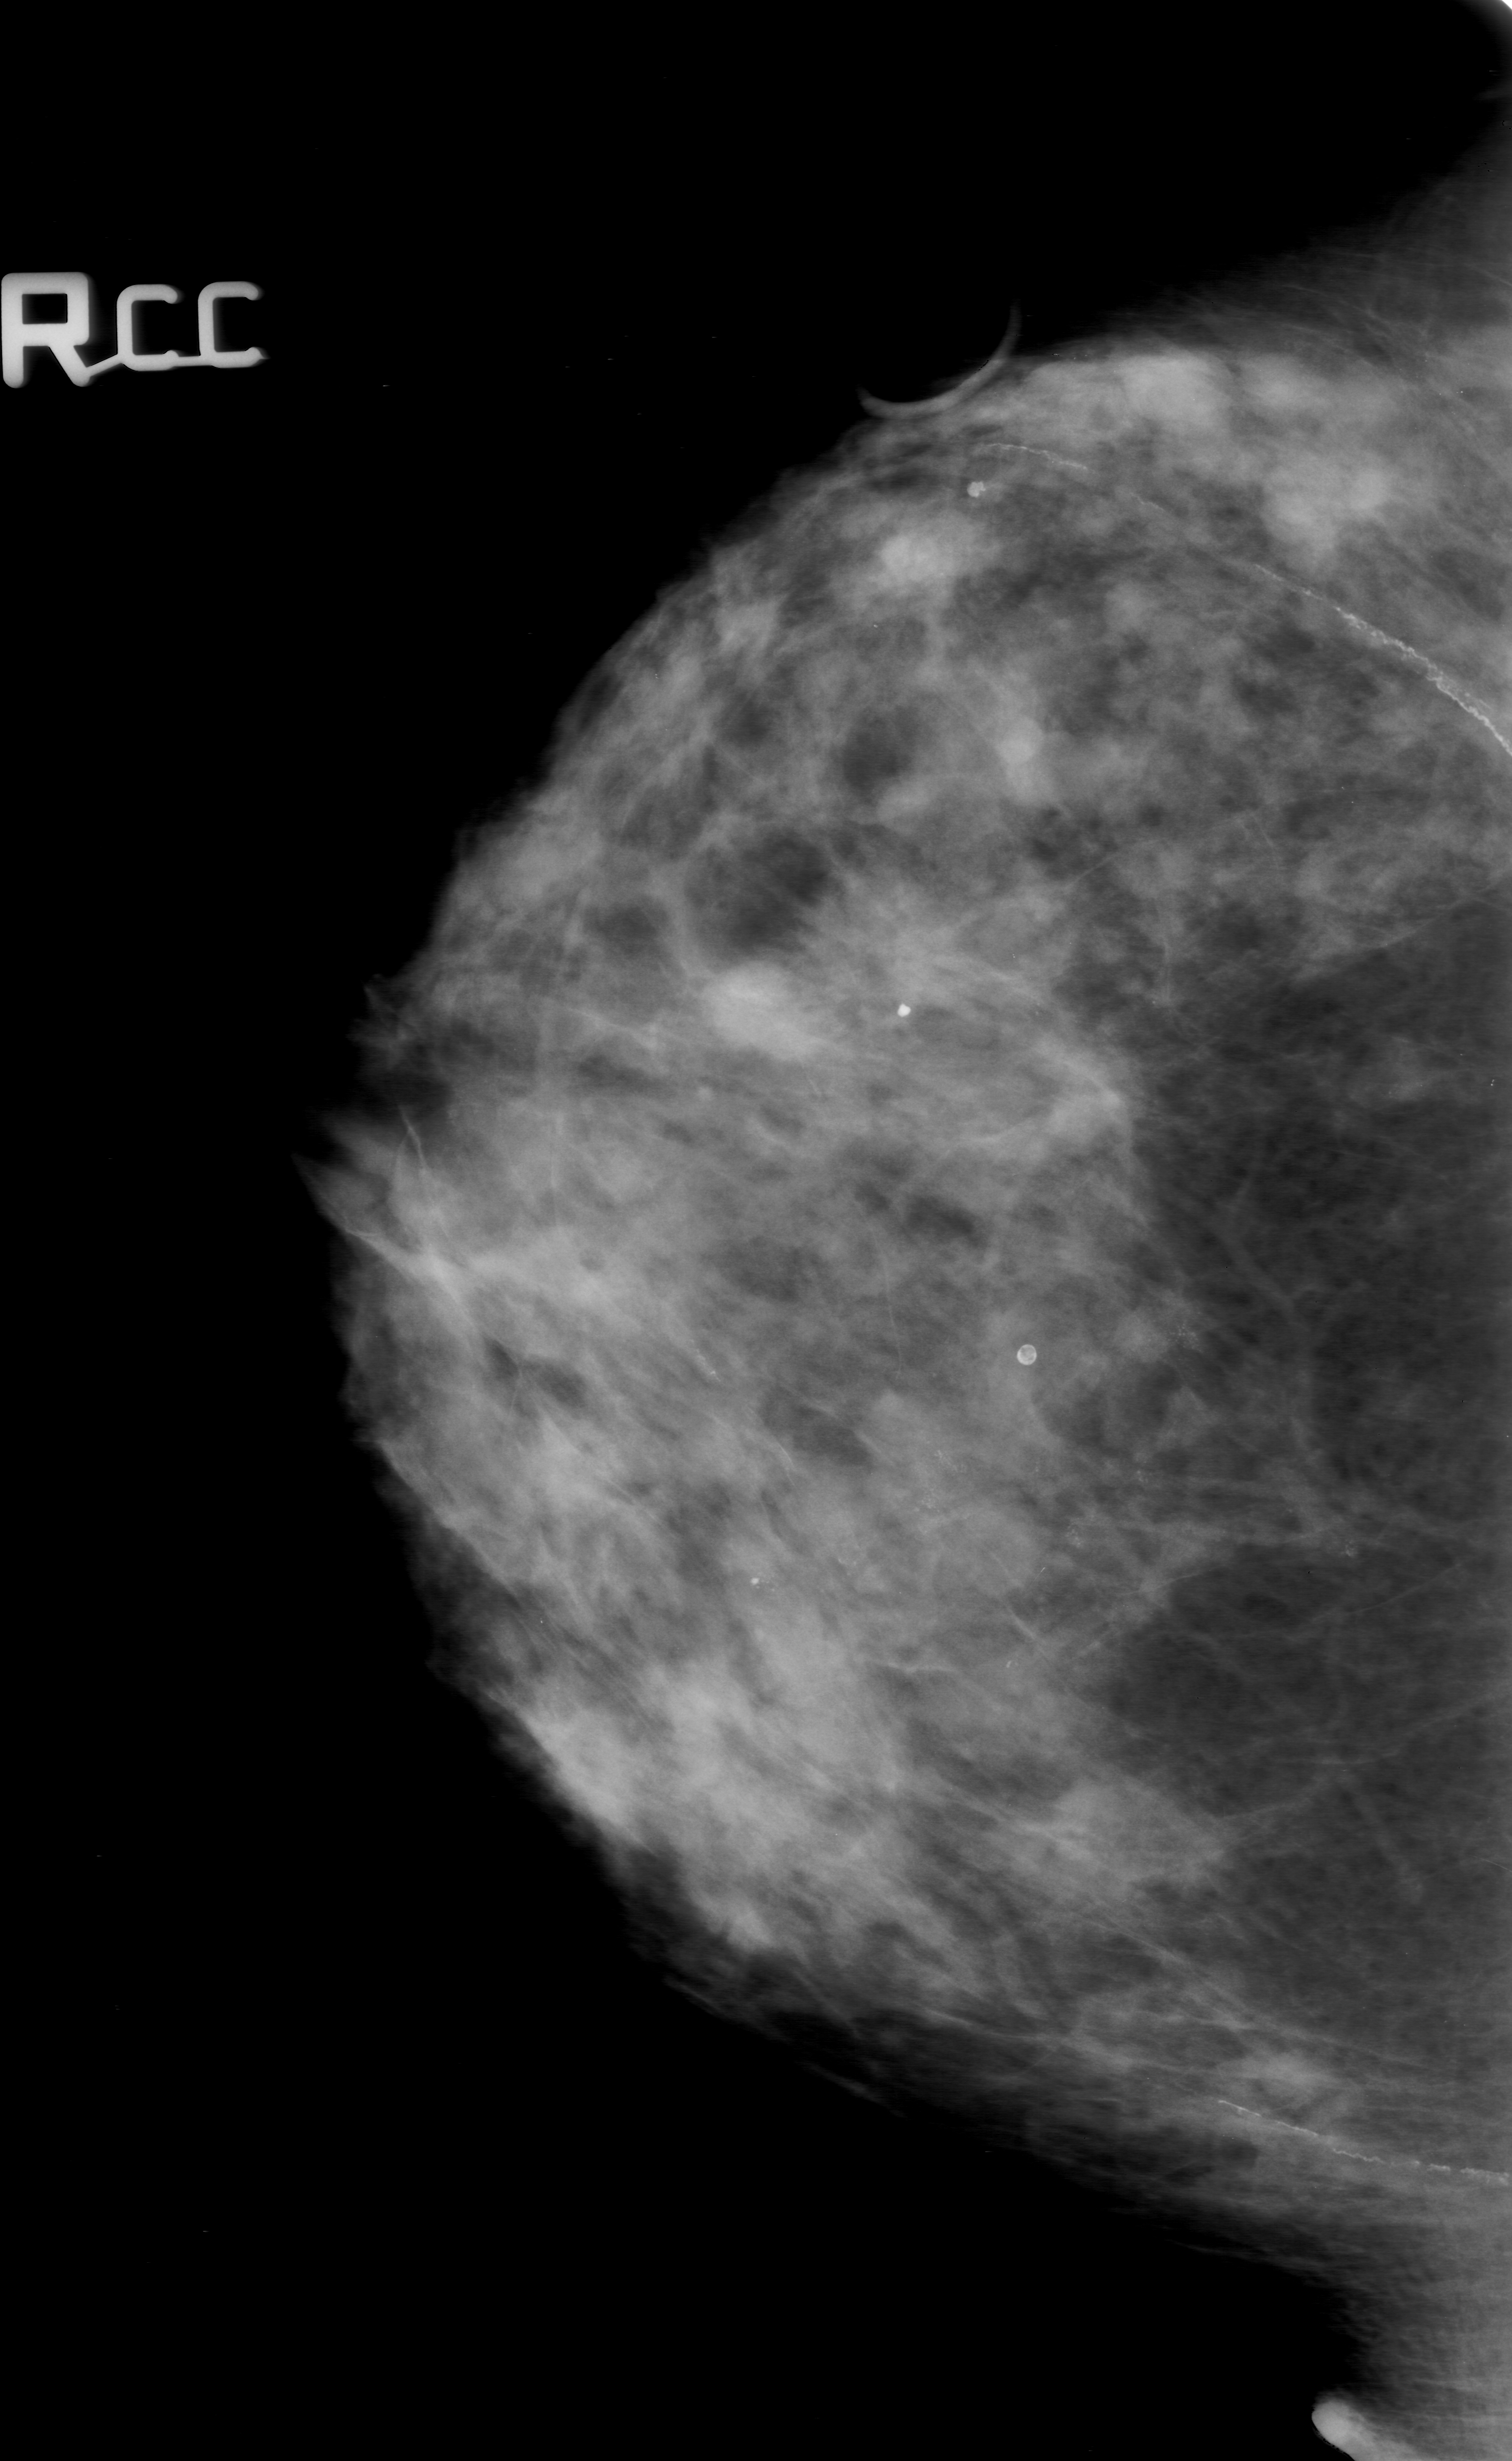
Digitized screen-film mammogram, right breast, craniocaudal (CC) view.
- Finding: calcifications, morphology amorphous, distribution segmental; BI-RADS assessment category 5; subtlety rating 3 on a 1 (subtle) to 5 (obvious) scale; pathology result (as recorded, not read from the image): malignant.